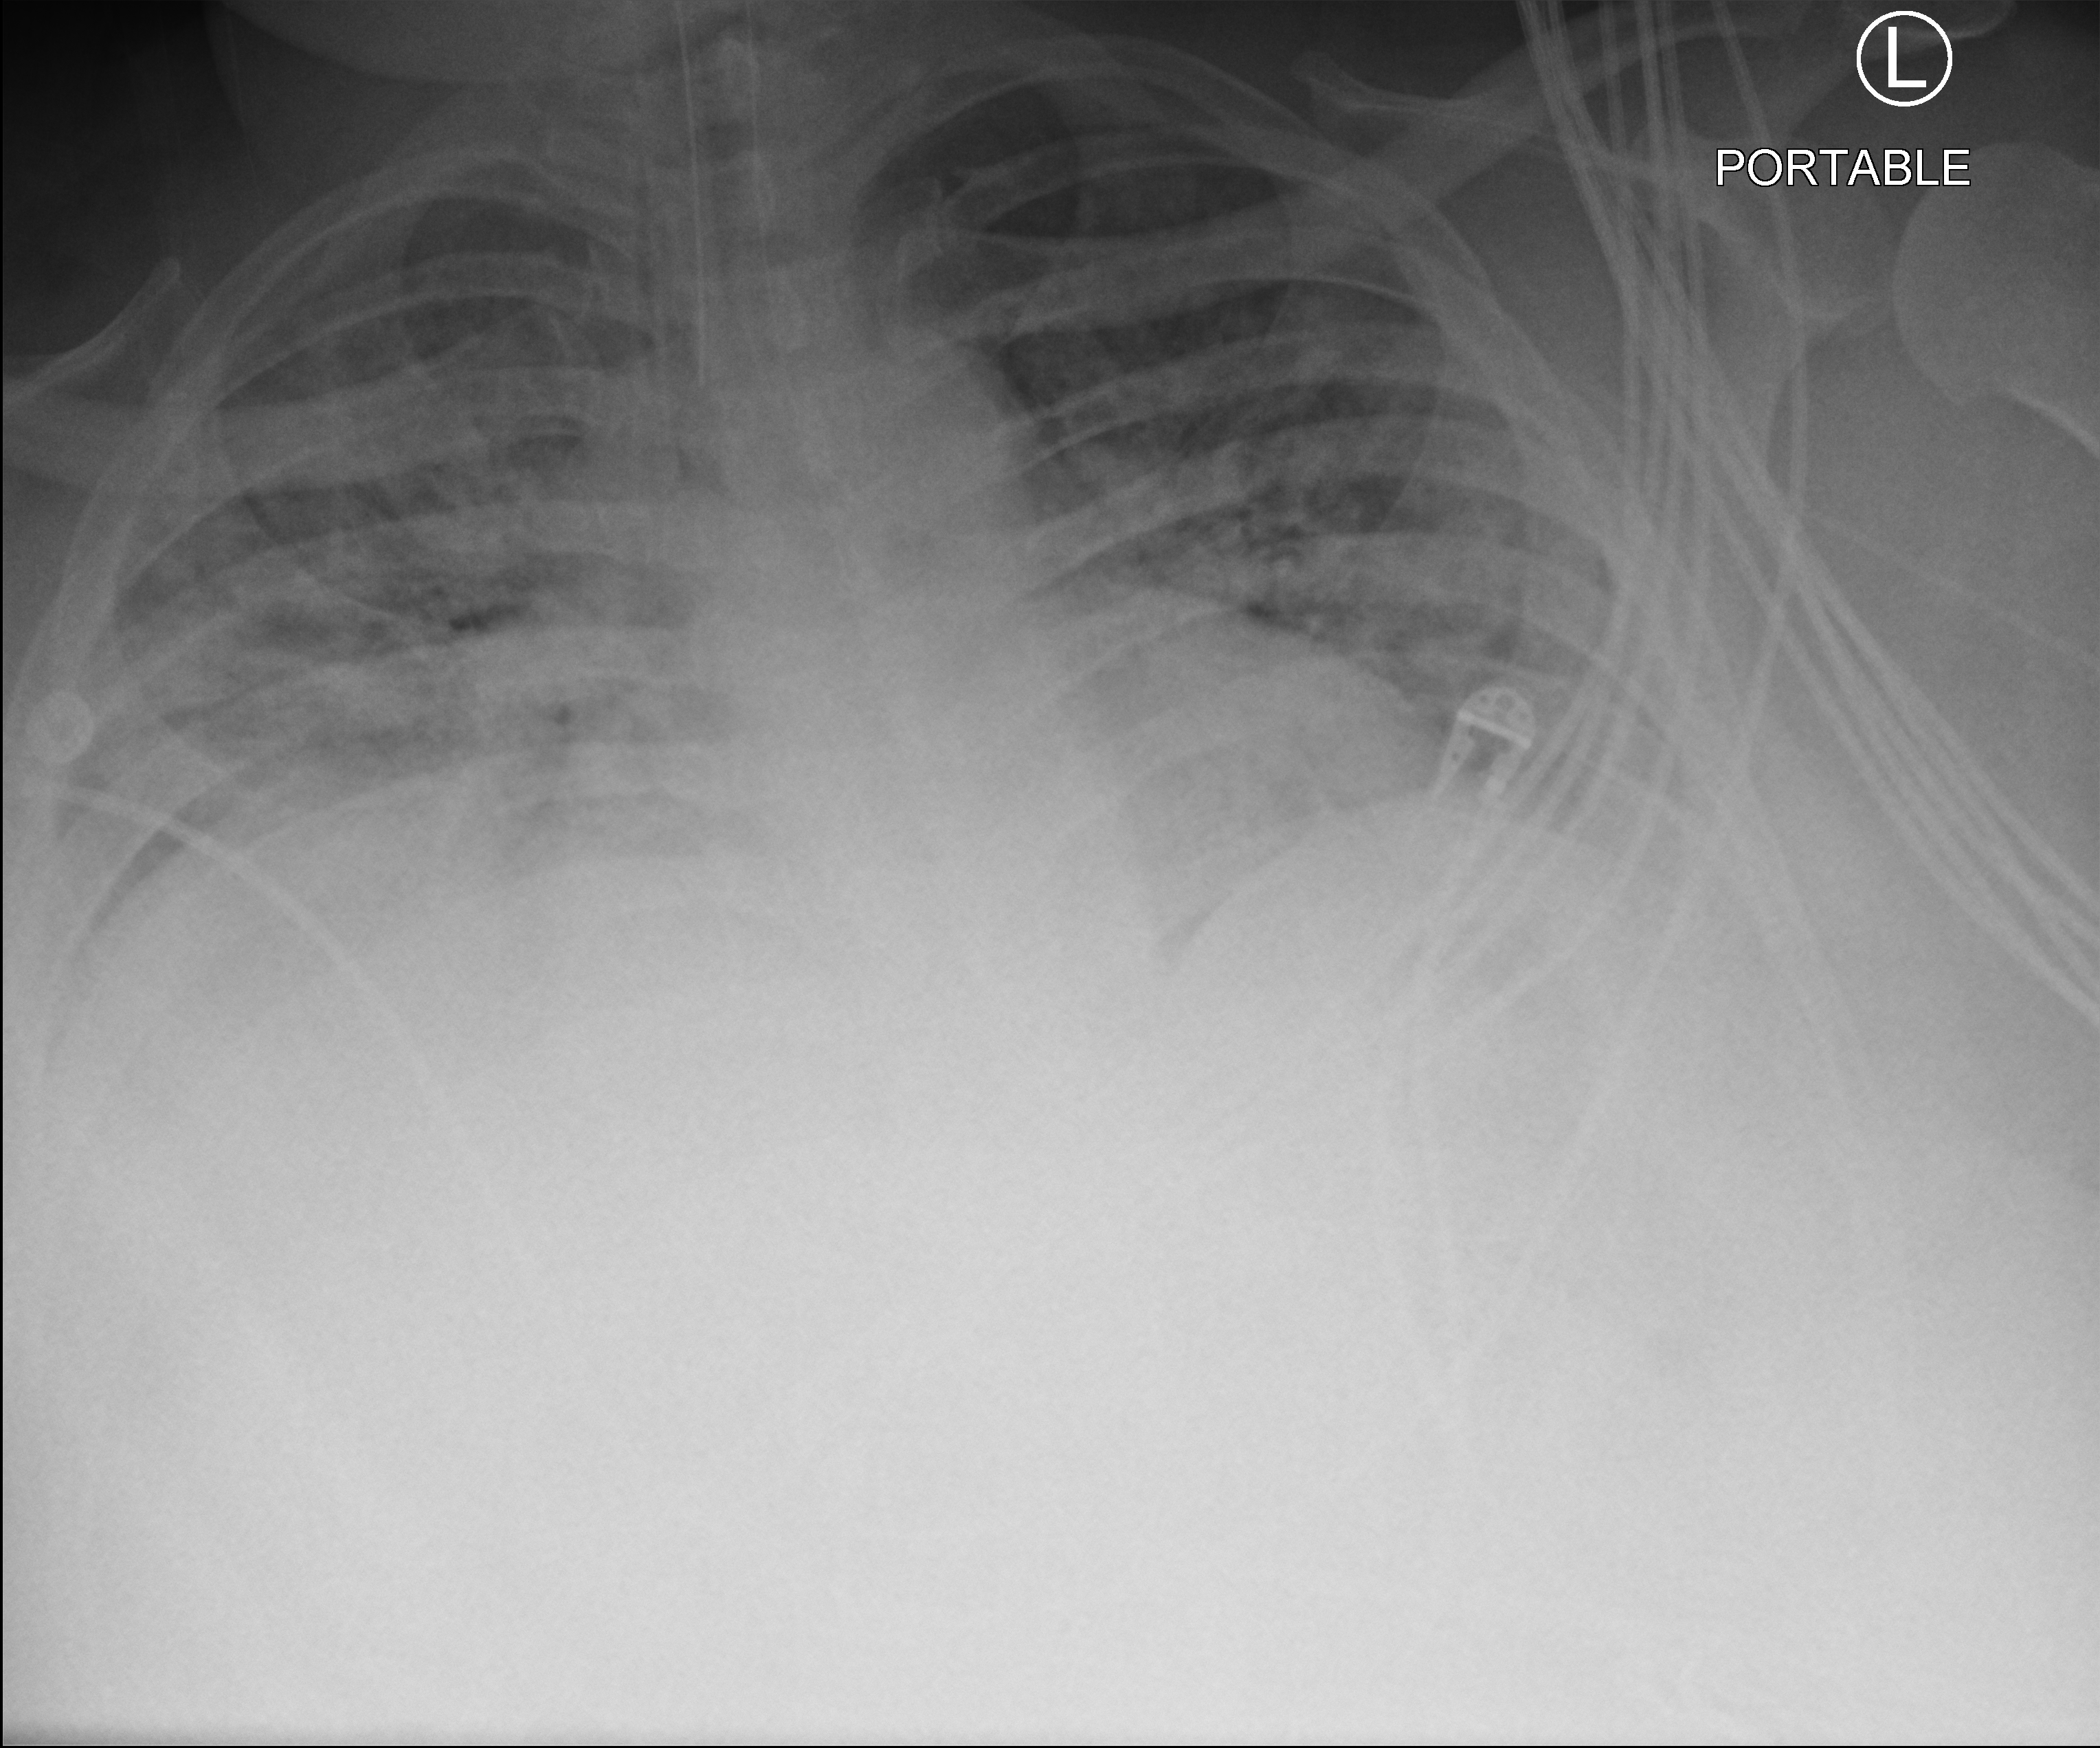
Bedside chest radiograph (computed radiography), anteroposterior (AP) projection. Male patient hospitalised with COVID-19, age 18–59 years.
From the hospital-stay record, not from the radiograph (when in the stay this image was taken is not recorded):
- diabetes (admission record): yes
- length of hospital stay: 69 days